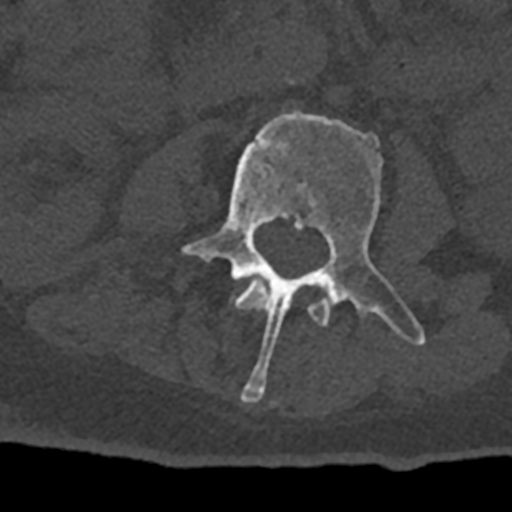
CT including the spine, one axial slice; position 323 of 797 along the scan axis; reconstruction kernel Br40s/3; bone window (W 1800 / L 400 HU); 512 × 512 image matrix. Patient: male, 74 years. From the clinical record (not read from this slice): primary cancer: renal; vertebrae with lytic lesions (as recorded): T10, L1, L2, L3, L4, L5.
Annotated regions visible in this slice (semi-automatic segmentation, software-assisted and operator-edited):
- L2 vertebra: box from (x=231, y=281) to (x=329, y=326) px
- L3 vertebra: (x=182, y=110)–(x=425, y=403)